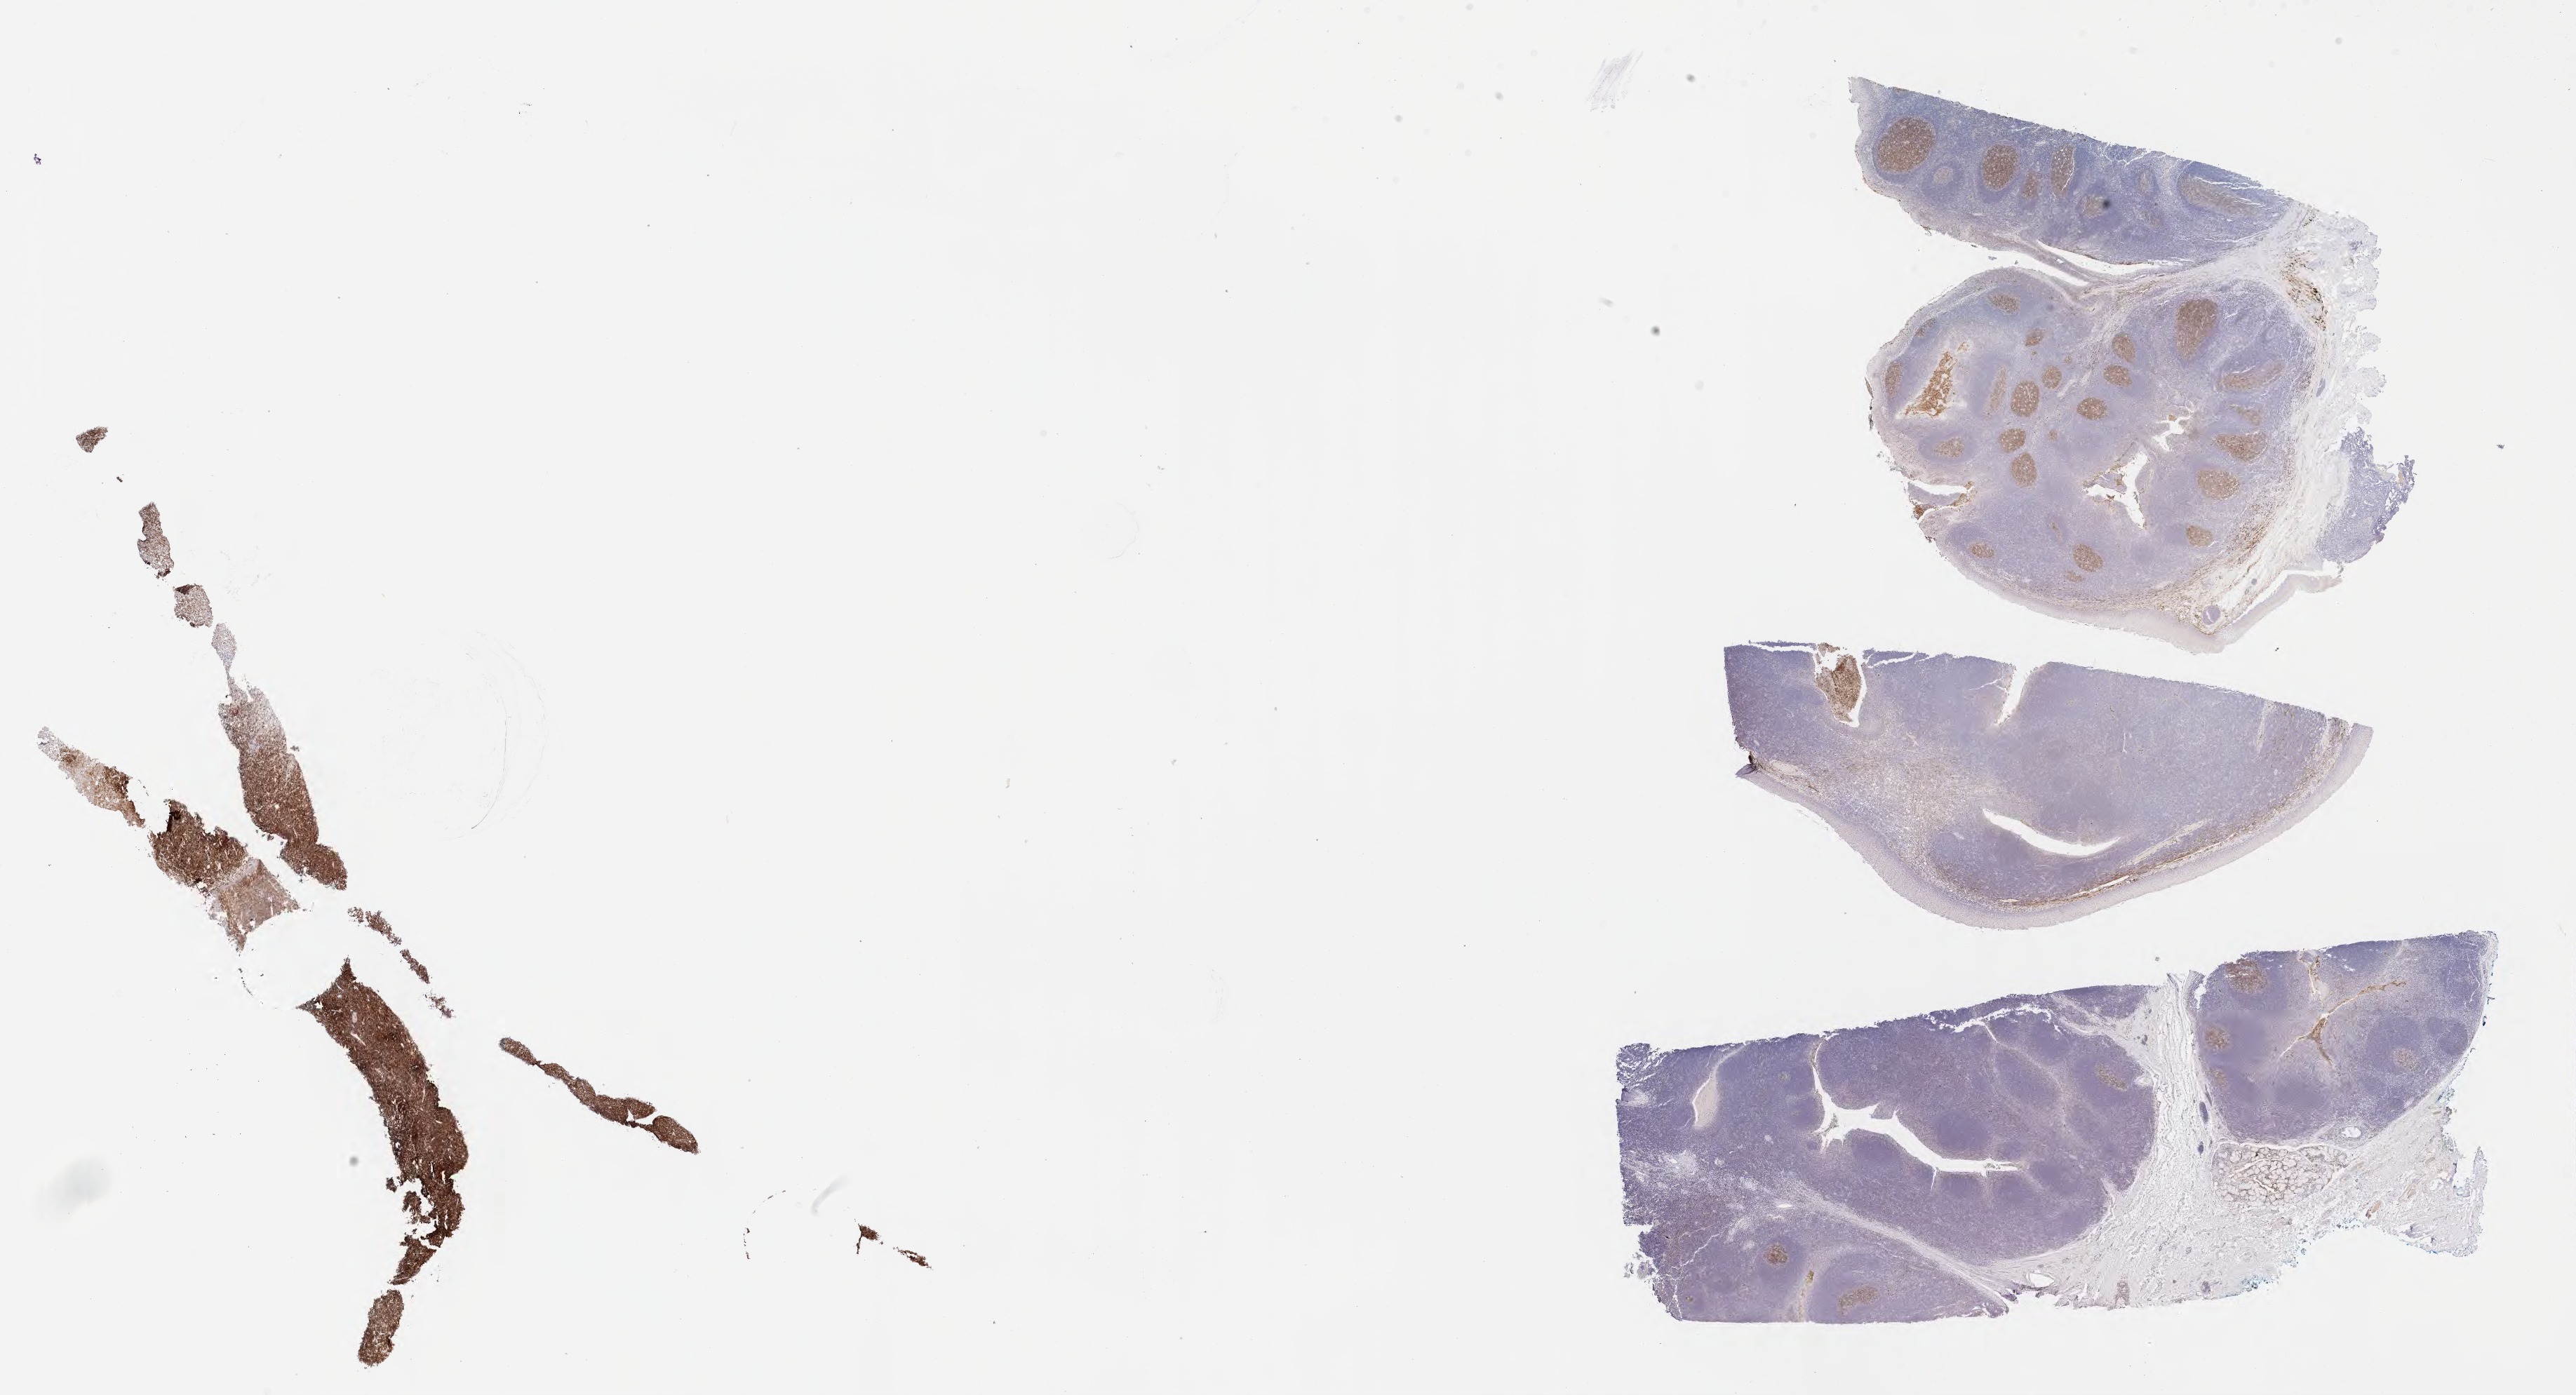
Immunohistochemistry (IHC) whole-slide image stained for CD10 — a low-resolution overview of the entire scanned area, about 29.7 x 16.1 mm; tumor tissue; anatomic site: abdomen proper. Patient: male, aged 14.
• diagnosis: Burkitt lymphoma, NOS